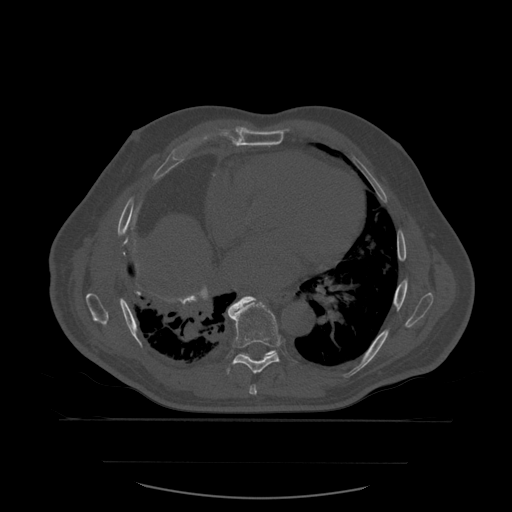
CT including the spine, one axial slice; position 359 of 590 along the scan axis; bone window (W 1800 / L 400 HU); 1.25 mm slice thickness; 512 × 512 image matrix. Patient age 71 years. From the clinical record (not read from this slice): primary cancer: lung; vertebrae with lytic lesions (as recorded): T1, T2, L5, S1.
Outlined on this slice (semi-automatically segmented with operator editing):
- T7 vertebra: bounding box [x1, y1, x2, y2] px = [249, 385, 258, 395]
- T8 vertebra: [227, 297, 281, 374]
- T9 vertebra: [265, 351, 275, 357]